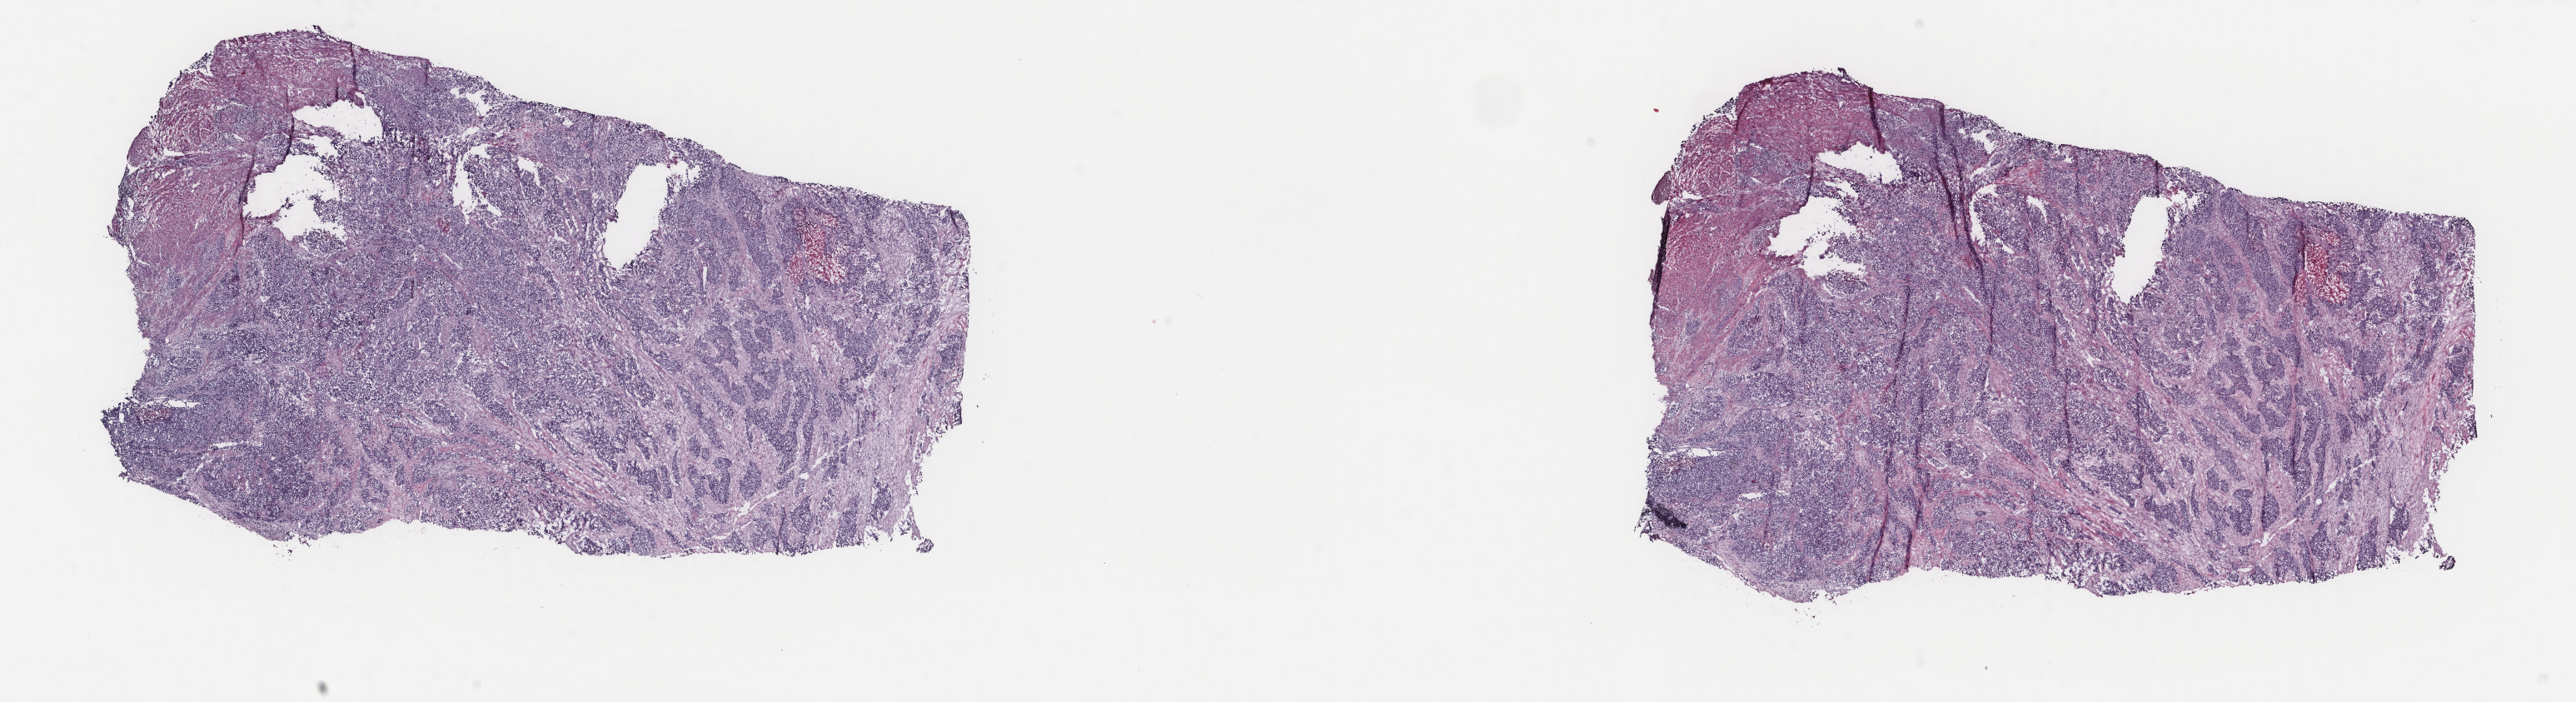
H&E whole-slide image — low-resolution overview of the scanned area, about 24.6 x 6.7 mm (acquisition: 40x scan). Frozen section from the top of the tissue portion. Cervix, primary tumour sample. Patient: female, age at initial diagnosis 51 years. Histologic grade: G2 (moderately differentiated). Composition of this section per pathologist review: tumour cells 85%, tumour nuclei 75%, normal cells 10%, stromal cells 0%, necrosis 5%. Inflammatory infiltration, as recorded: lymphocyte infiltration 2%, monocyte infiltration 0%, neutrophil infiltration 0%.
FIGO stage: IIA2. Pathologic diagnosis: Squamous cell carcinoma, NOS (cervix uteri).